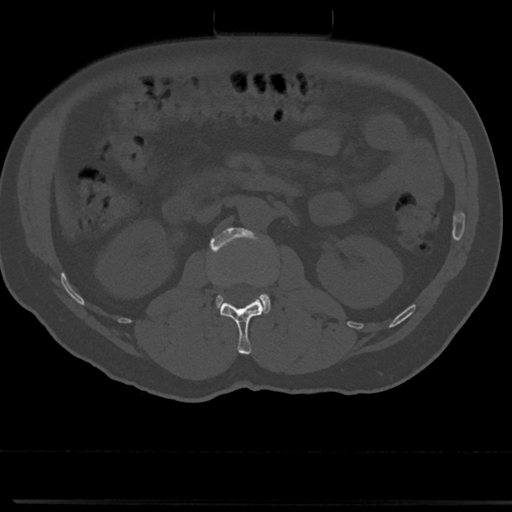
CT including the spine, one axial slice; position 50 of 817 along the scan axis; bone window (W 1800 / L 400 HU); 0.5 mm slice thickness; 512 × 512 image matrix. Patient: male, 61 years. From the clinical record (not read from this slice): primary cancer: prostate.
Annotated regions visible in this slice (semi-automatically segmented with operator editing):
- L1 vertebra: bounding box [x1, y1, x2, y2] px = [219, 298, 264, 355]
- L2 vertebra: [209, 227, 271, 314]